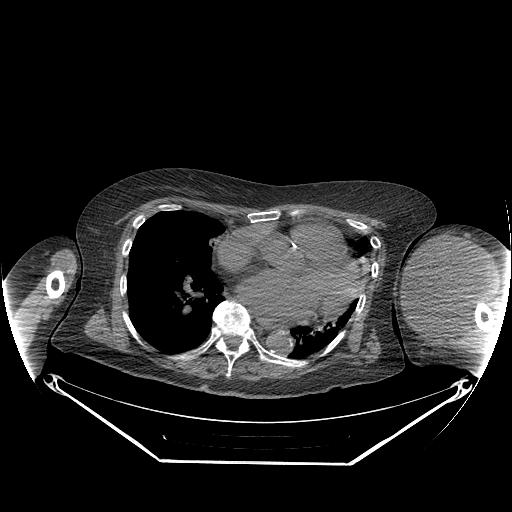
CT of an extremity soft-tissue mass (from a PET/CT study), one axial slice; slice 164 of 267 in the series (ordered by position); reconstruction kernel STANDARD; soft-tissue window (W 400 / L 40 HU); 3.75 mm slice thickness; 512 × 512 image matrix, field of view 500 × 500 mm. Female patient. From the clinical record (not read from this slice): histological type: pleiomorphic leiomyosarcoma; grade: high; site of the primary tumour: left biceps.
Annotated regions visible in this slice (expert contour drawn on MRI and transferred to this co-registered scan by the dataset authors):
- gross tumour volume including surrounding oedema: bounding box [x1, y1, x2, y2] px = [402, 235, 490, 330]
- gross tumour volume (mass): [402, 235, 489, 328]